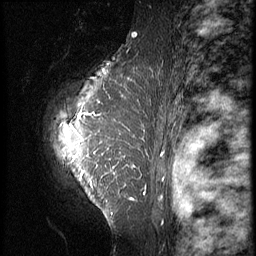
Breast MRI (dynamic contrast-enhanced), one sagittal slice. Position 49 of 64 along the scan axis. 3 images stored at this slice position (order not interpretable as contrast timing). 1.5 T. TE 4.2 ms, TR 9 ms. 256 × 256 image matrix, field of view 180 × 180 mm. Patient: female, 39 years. From the clinical record (not read from this slice): setting: breast cancer imaged before/during neoadjuvant chemotherapy; receptor status: HER2-positive.
Annotated regions visible in this slice (semi-automatic segmentation, software-assisted and operator-edited):
- analysis volume of interest (the breast-tissue region the enhancement analysis was run in; not a lesion): bounding box <43,47,149,239> (left, top, right, bottom; pixels)
- tumour enhancement mask (voxels above the 140 % enhancement threshold inside the analysis volume of interest): <60,114,145,199>